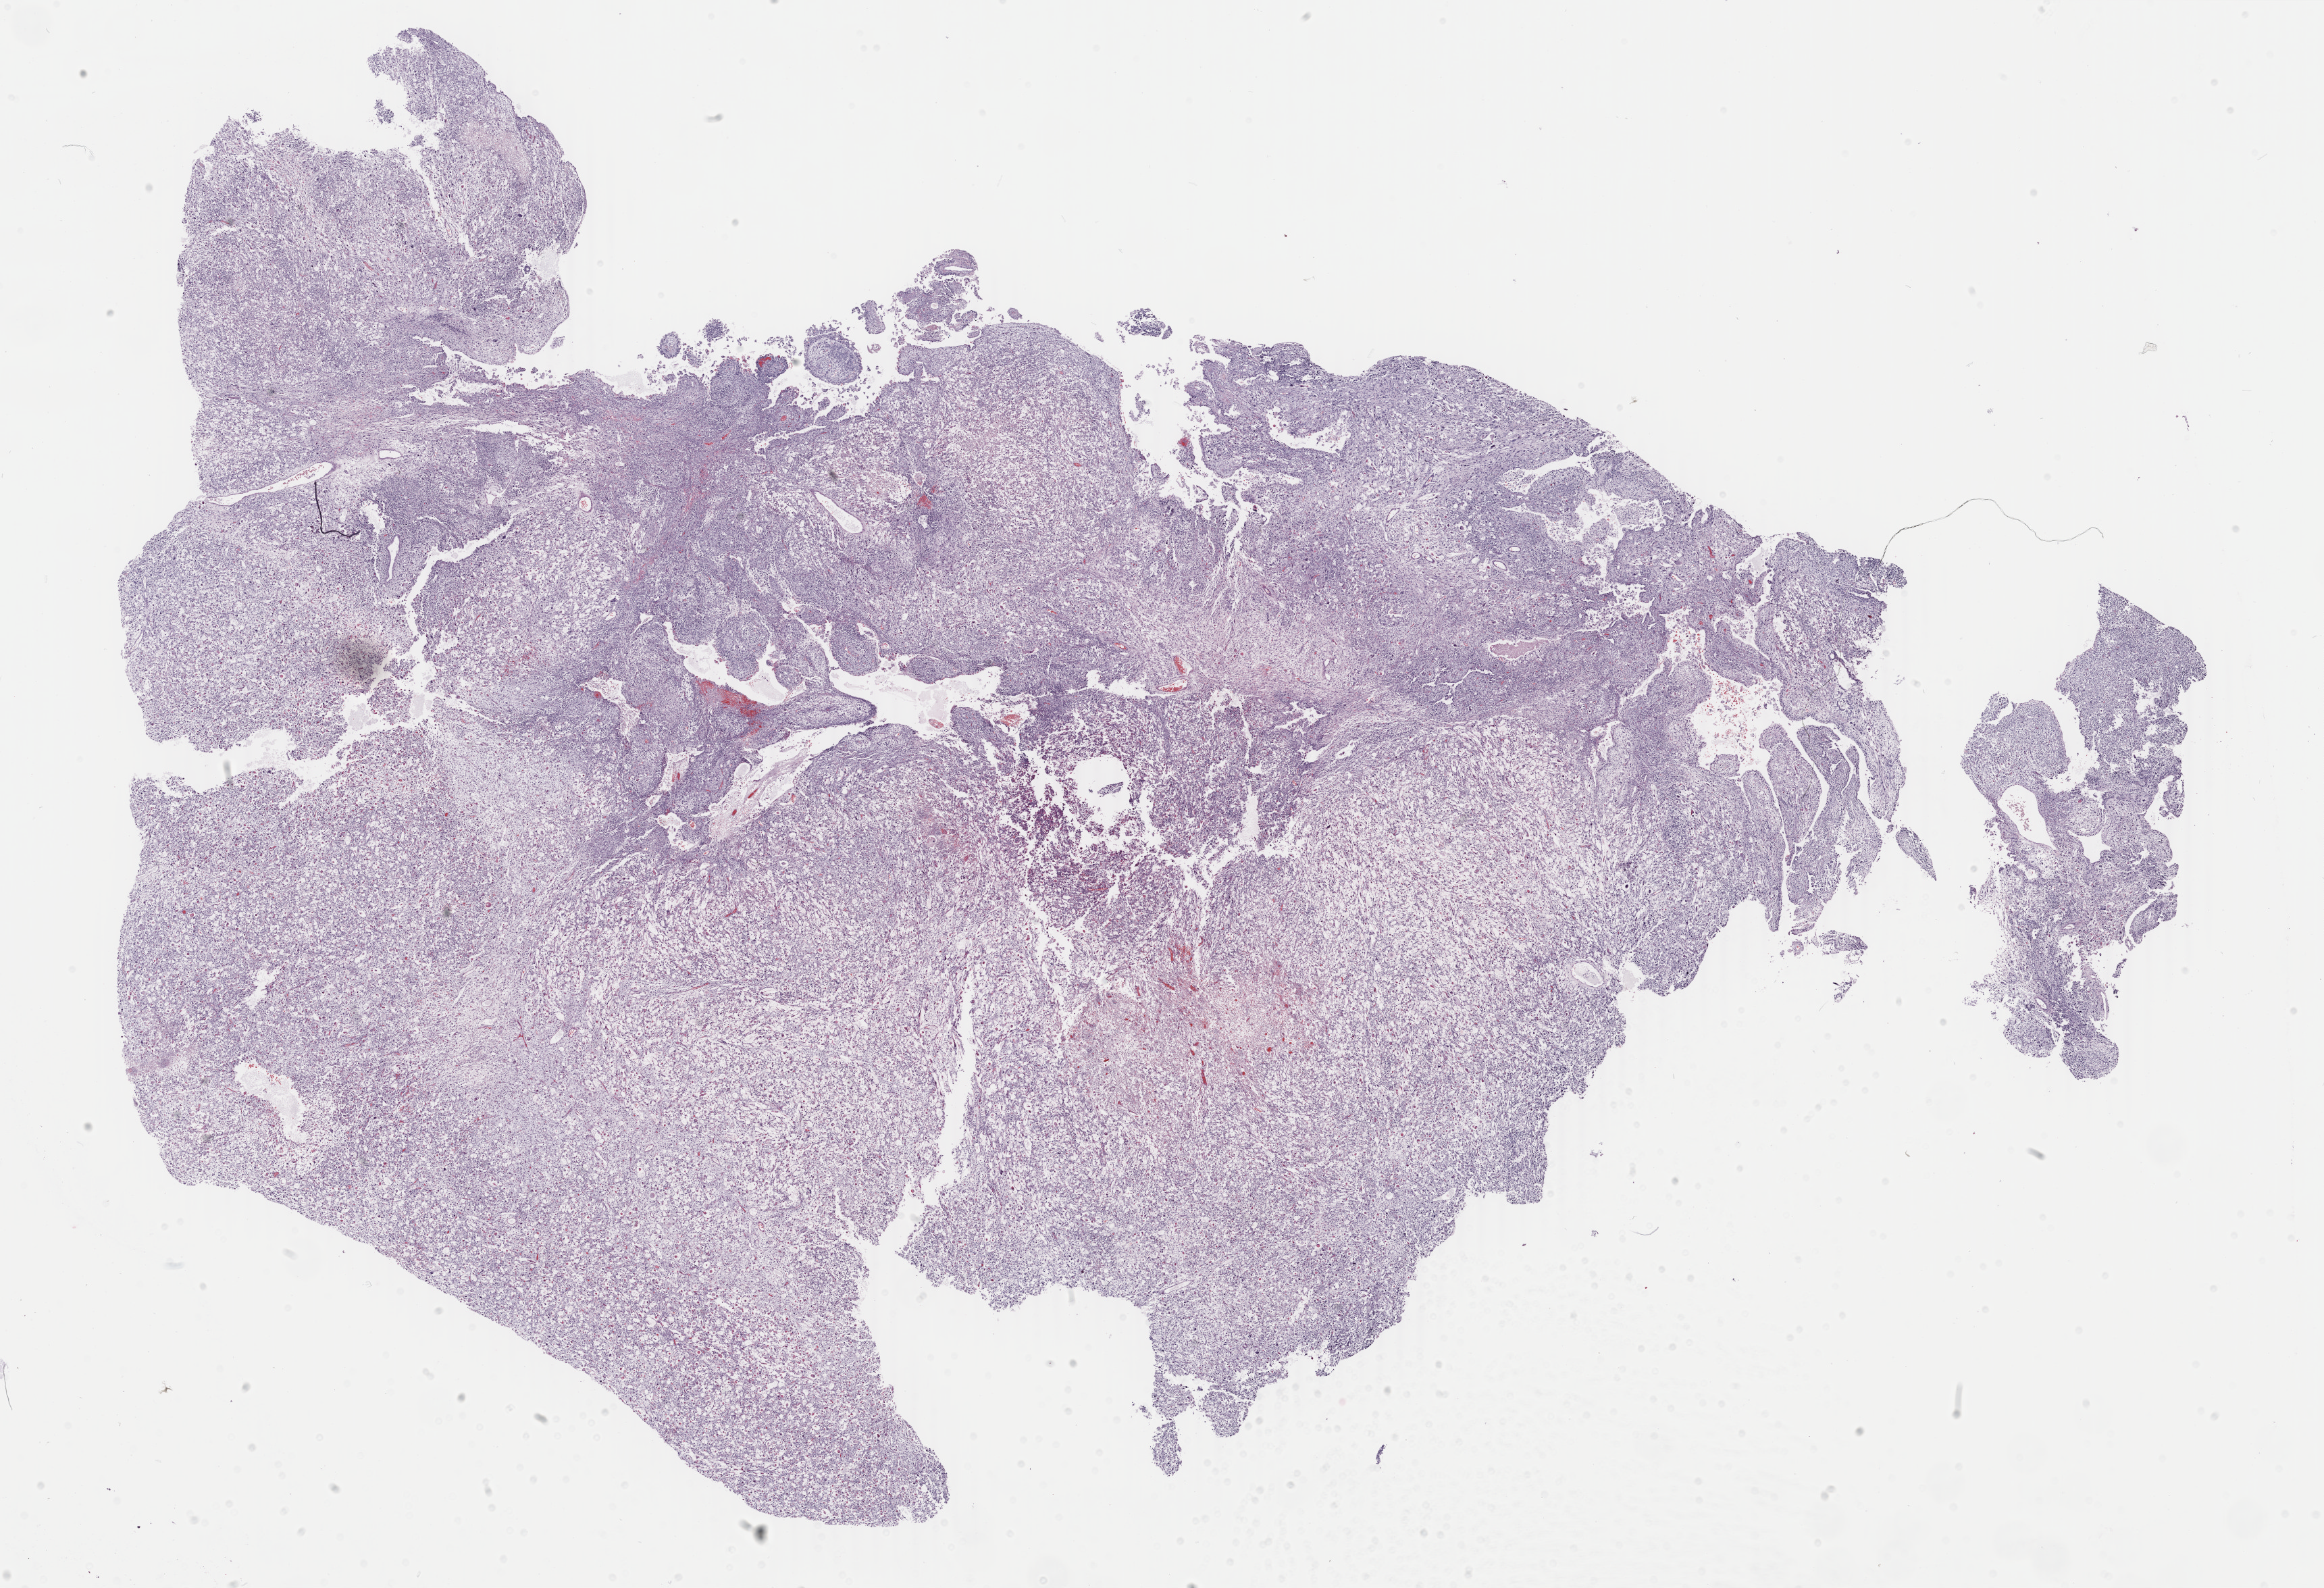
Digitized H&E tissue section (whole slide) — a low-resolution overview of the entire scanned area, about 27.4 x 18.7 mm; formalin-fixed paraffin-embedded (FFPE) diagnostic section; primary tumour sample from the uterus. Female, age 65 years at initial diagnosis.
• FIGO stage: IA
• pathologic diagnosis: Mullerian mixed tumor